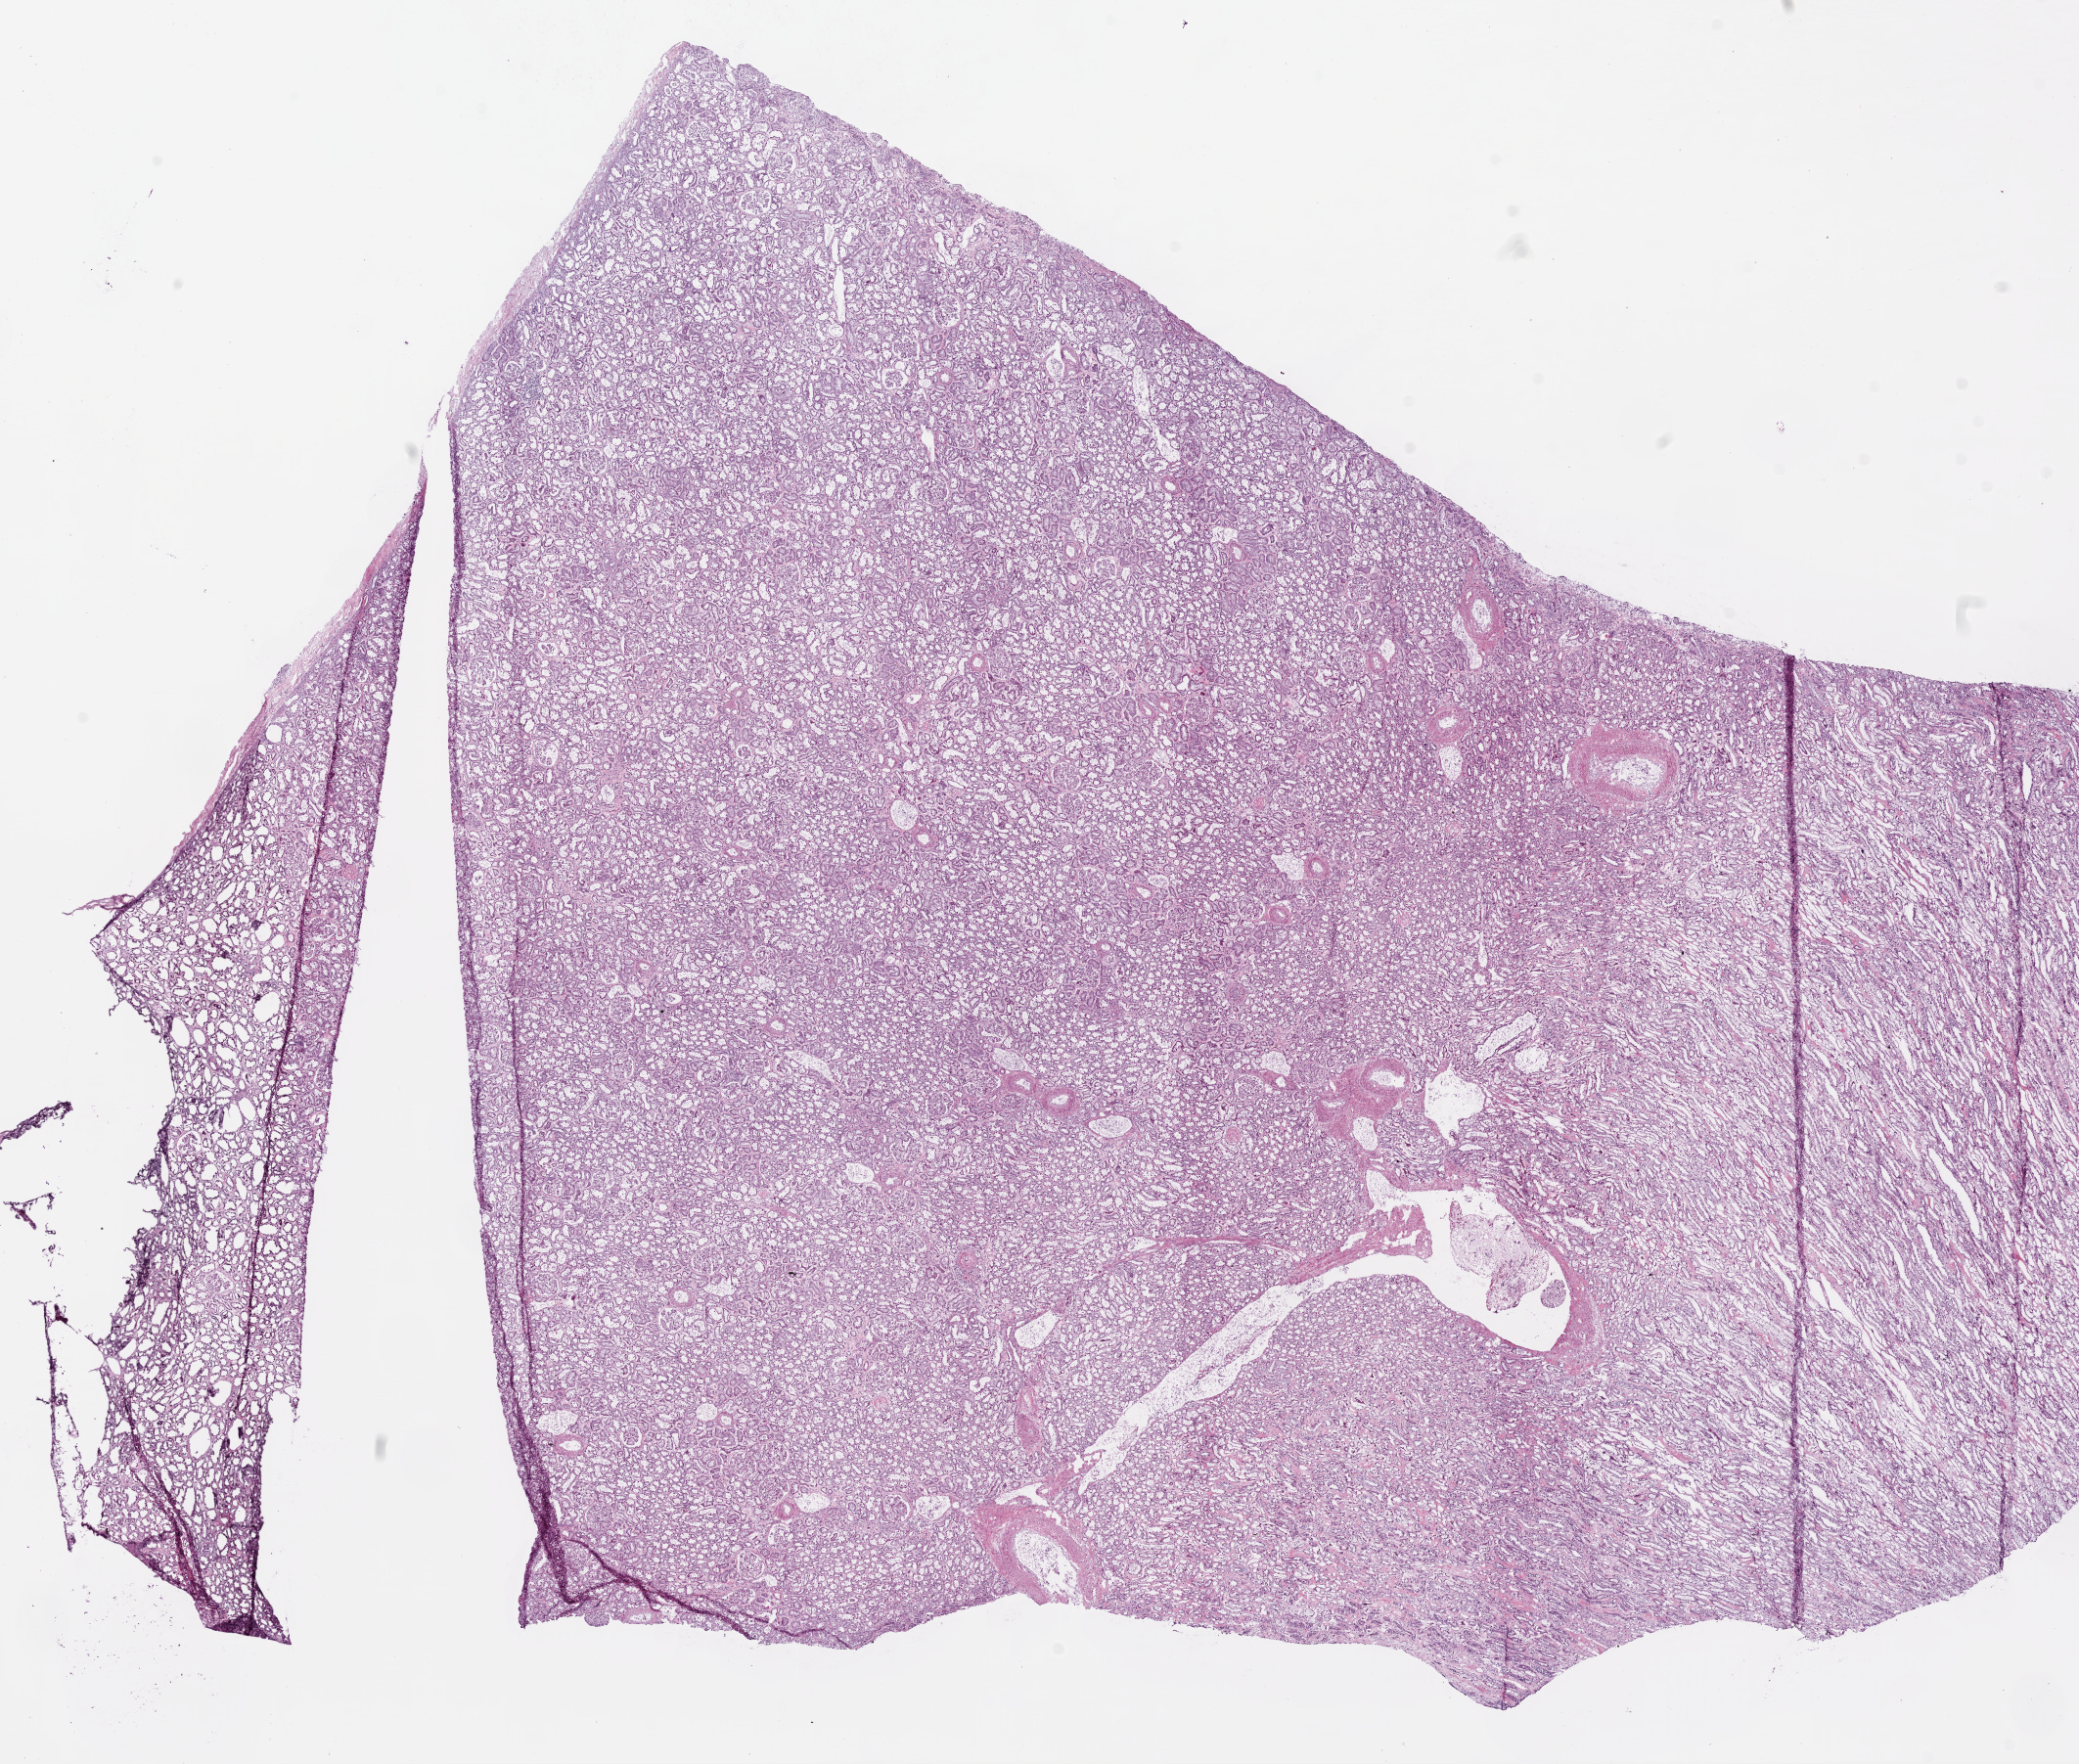
Whole-slide histology image, H&E — low-resolution overview of the scanned area, about 17.1 x 14.5 mm; frozen section from the bottom of the tissue portion; solid tissue normal (non-tumour tissue) sample from the kidney. Male, age 57 years at initial diagnosis.
* this section: solid tissue normal sample (biorepository sample class)
* patient diagnosis: Clear cell adenocarcinoma, NOS